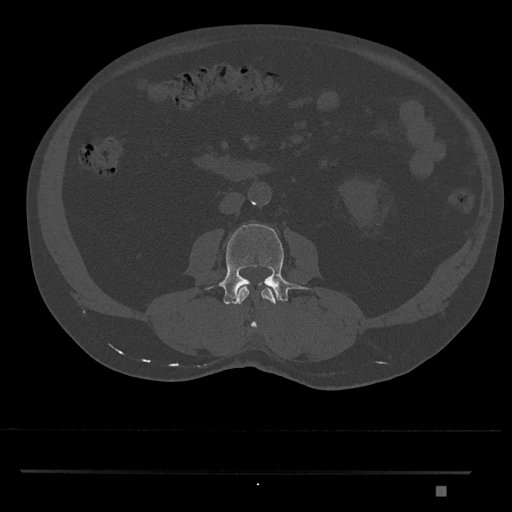
CT including the spine, one axial slice; slice 700 of 1134 in the series (ordered by position); reconstruction kernel Br40s/3; 120 kVp; bone window (W 1800 / L 400 HU); 512 × 512 image matrix, field of view 429 × 429 mm. Male patient, age 65 years. Case-level facts recorded for this patient, not image findings: primary cancer: prostate.
Outlined on this slice (semi-automatic segmentation, software-assisted and operator-edited):
- L2 vertebra: box from (x=237, y=286) to (x=276, y=328) px
- L3 vertebra: (x=206, y=224)–(x=309, y=304)